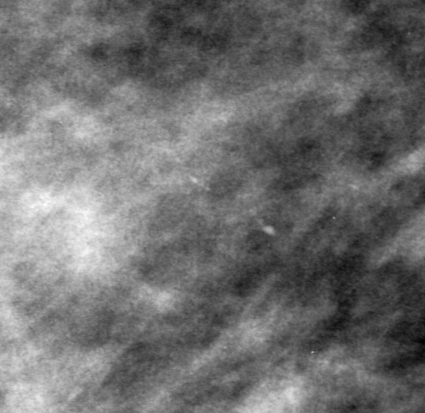
Cropped region of a digitized screen-film mammogram centred on a radiologist-marked abnormality; right breast; MLO view; BI-RADS breast density category 3 (scale 1–4).
Finding: calcifications, morphology punctate, distribution clustered; BI-RADS assessment category 0; pathology result (as recorded, not read from the image): malignant.